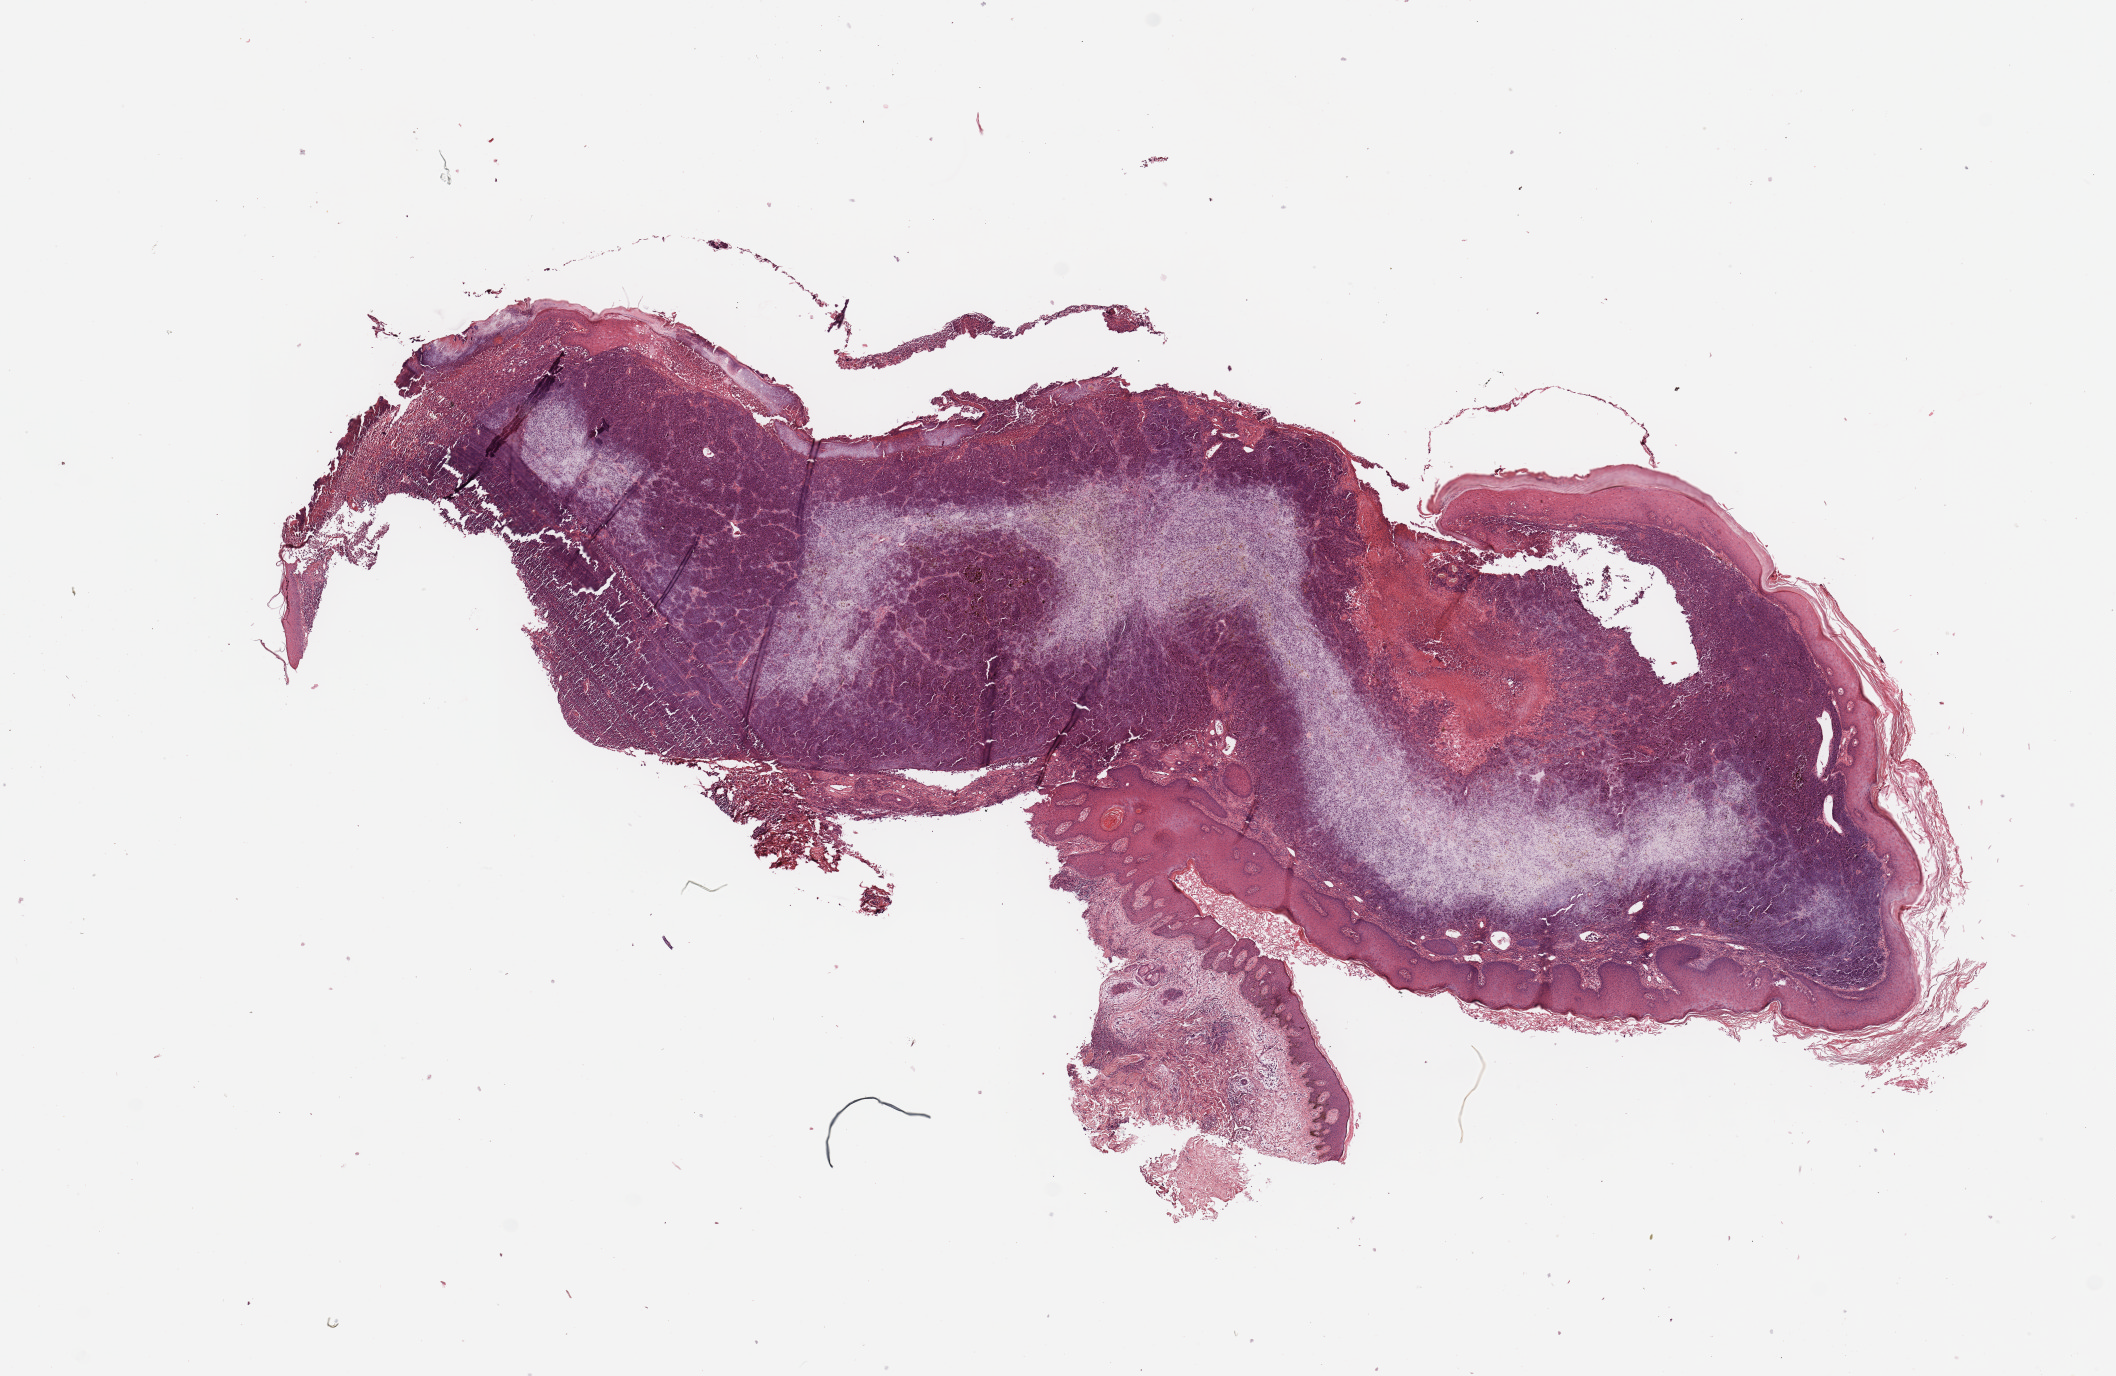
H&E whole-slide image — shown as a low-resolution overview of the whole scanned area (about 16.7 x 10.9 mm, slide scanned at 20x). Tumour tissue sample, sampled site: skin. Male, 59 y/o.
Histologic diagnosis: Malignant melanoma, NOS.